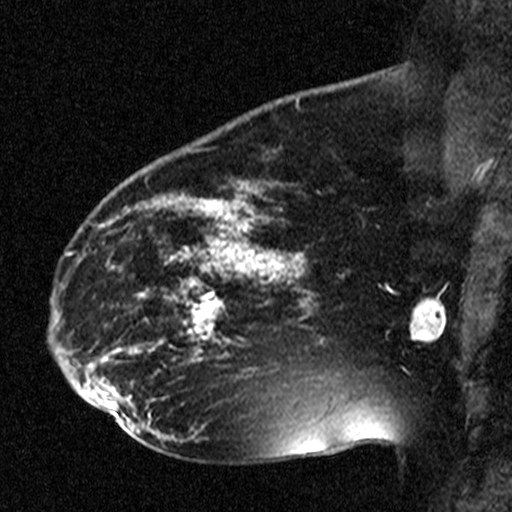
Breast MRI (dynamic contrast-enhanced), one sagittal slice. Slice 29 of 44 in the series (ordered by position). Dynamic contrast-enhanced study with each time point stored as its own series, time point 2 of 3 at this slice position (early post-contrast, ordered by acquisition time). 1.5 T. TE 4.5 ms, TR 11 ms. 3 mm slice thickness. 512 × 512 image matrix, field of view 200 × 200 mm. Patient: female, 38 years. Case-level facts recorded for this patient, not image findings: setting: breast cancer imaged before/during neoadjuvant chemotherapy; receptor status: HR-positive, HER2-negative.
Annotated regions visible in this slice (semi-automatic segmentation, software-assisted and operator-edited):
- analysis volume of interest (the breast-tissue region the enhancement analysis was run in; not a lesion): box from (x=176, y=272) to (x=251, y=349) px
- tumour enhancement mask (voxels above the 90 % enhancement threshold inside the analysis volume of interest): (x=178, y=272)–(x=250, y=345)